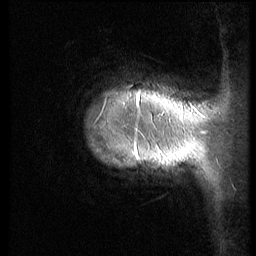
Breast MRI (dynamic contrast-enhanced), one sagittal slice; position 8 of 70 along the scan axis; 3 images stored at this slice position (order not interpretable as contrast timing); 1.5 T; TE 4.2 ms, TR 9 ms; 2.5 mm slice thickness; 256 × 256 image matrix, field of view 180 × 180 mm. Female patient, age 28 years. From the clinical record (not read from this slice): setting: breast cancer imaged before/during neoadjuvant chemotherapy.
Outlined on this slice (semi-automatically segmented with operator editing):
- analysis volume of interest (the breast-tissue region the enhancement analysis was run in; not a lesion): bounding box [x1, y1, x2, y2] px = [82, 55, 186, 204]
- tumour enhancement mask (voxels above the 140 % enhancement threshold inside the analysis volume of interest): [138, 98, 140, 102]